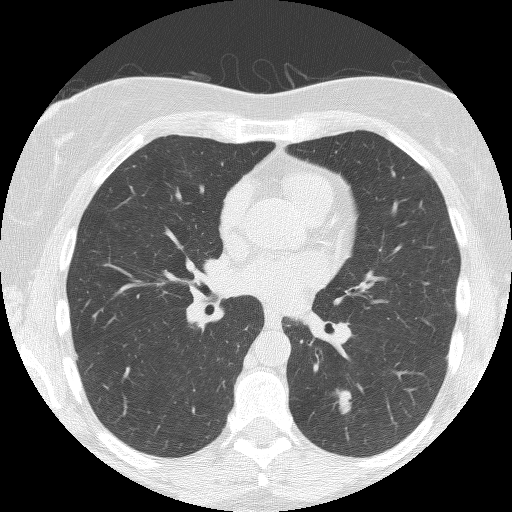
Axial slice from a low-dose chest CT screening exam; second screening round (one year after baseline); lung window (W 1500 / L -600 HU); 2.5 mm slice thickness; lung (sharp) reconstruction kernel (BONE); 120 kVp; 512 × 512 image matrix, field of view 300 × 300 mm. Female participant, aged 60 years at enrolment. Former smoker at enrolment.
Lesion marked by an expert reader, box from (x=318, y=382) to (x=360, y=424) px. Screening reader's record for this exam (one nodule recorded; not confirmed to be the boxed lesion): non-calcified nodule or mass ≥4 mm, left lower lobe, 16 × 7 mm, smooth margins, soft tissue attenuation, pre-existing on the prior screen: no. Lung cancer was diagnosed 54 days after this screen: small cell carcinoma, NOS, left lower lobe, stage IIA (AJCC 6th edition), 12 mm at pathology.